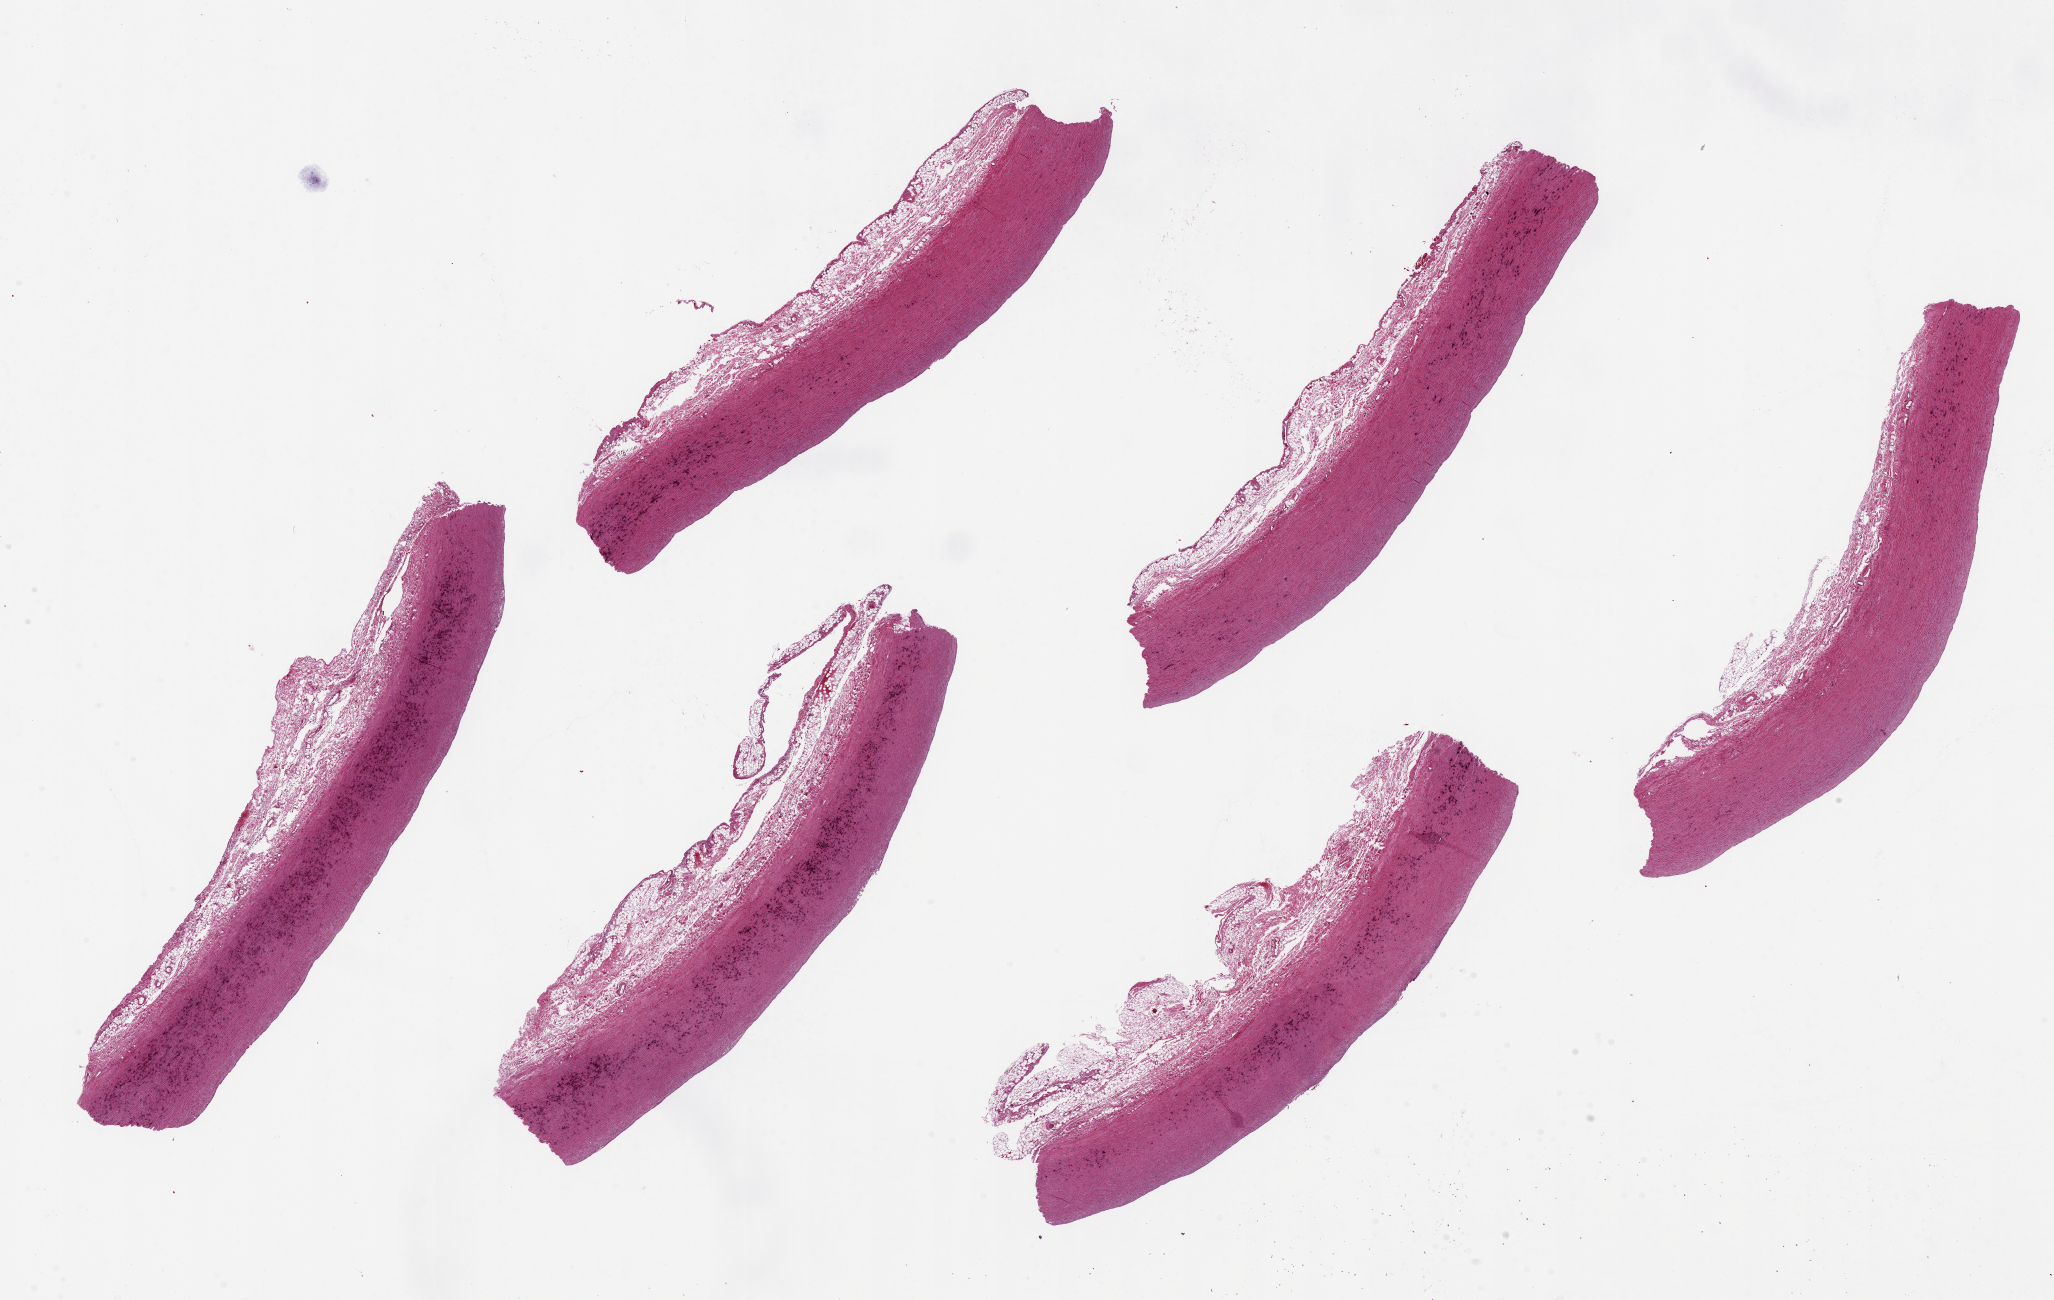
Digitized haematoxylin and eosin-stained section, shown as a low-resolution overview of the whole scanned area (about 32.5 x 20.6 mm, slide scanned at 20x); PAXgene-fixed paraffin-embedded (PFPE) section; target tissue: aorta; tissue donor sample.
Pathologist's review note for this sample: 6 pieces, up to 11.3x2 mm; dispersed medial calcification.